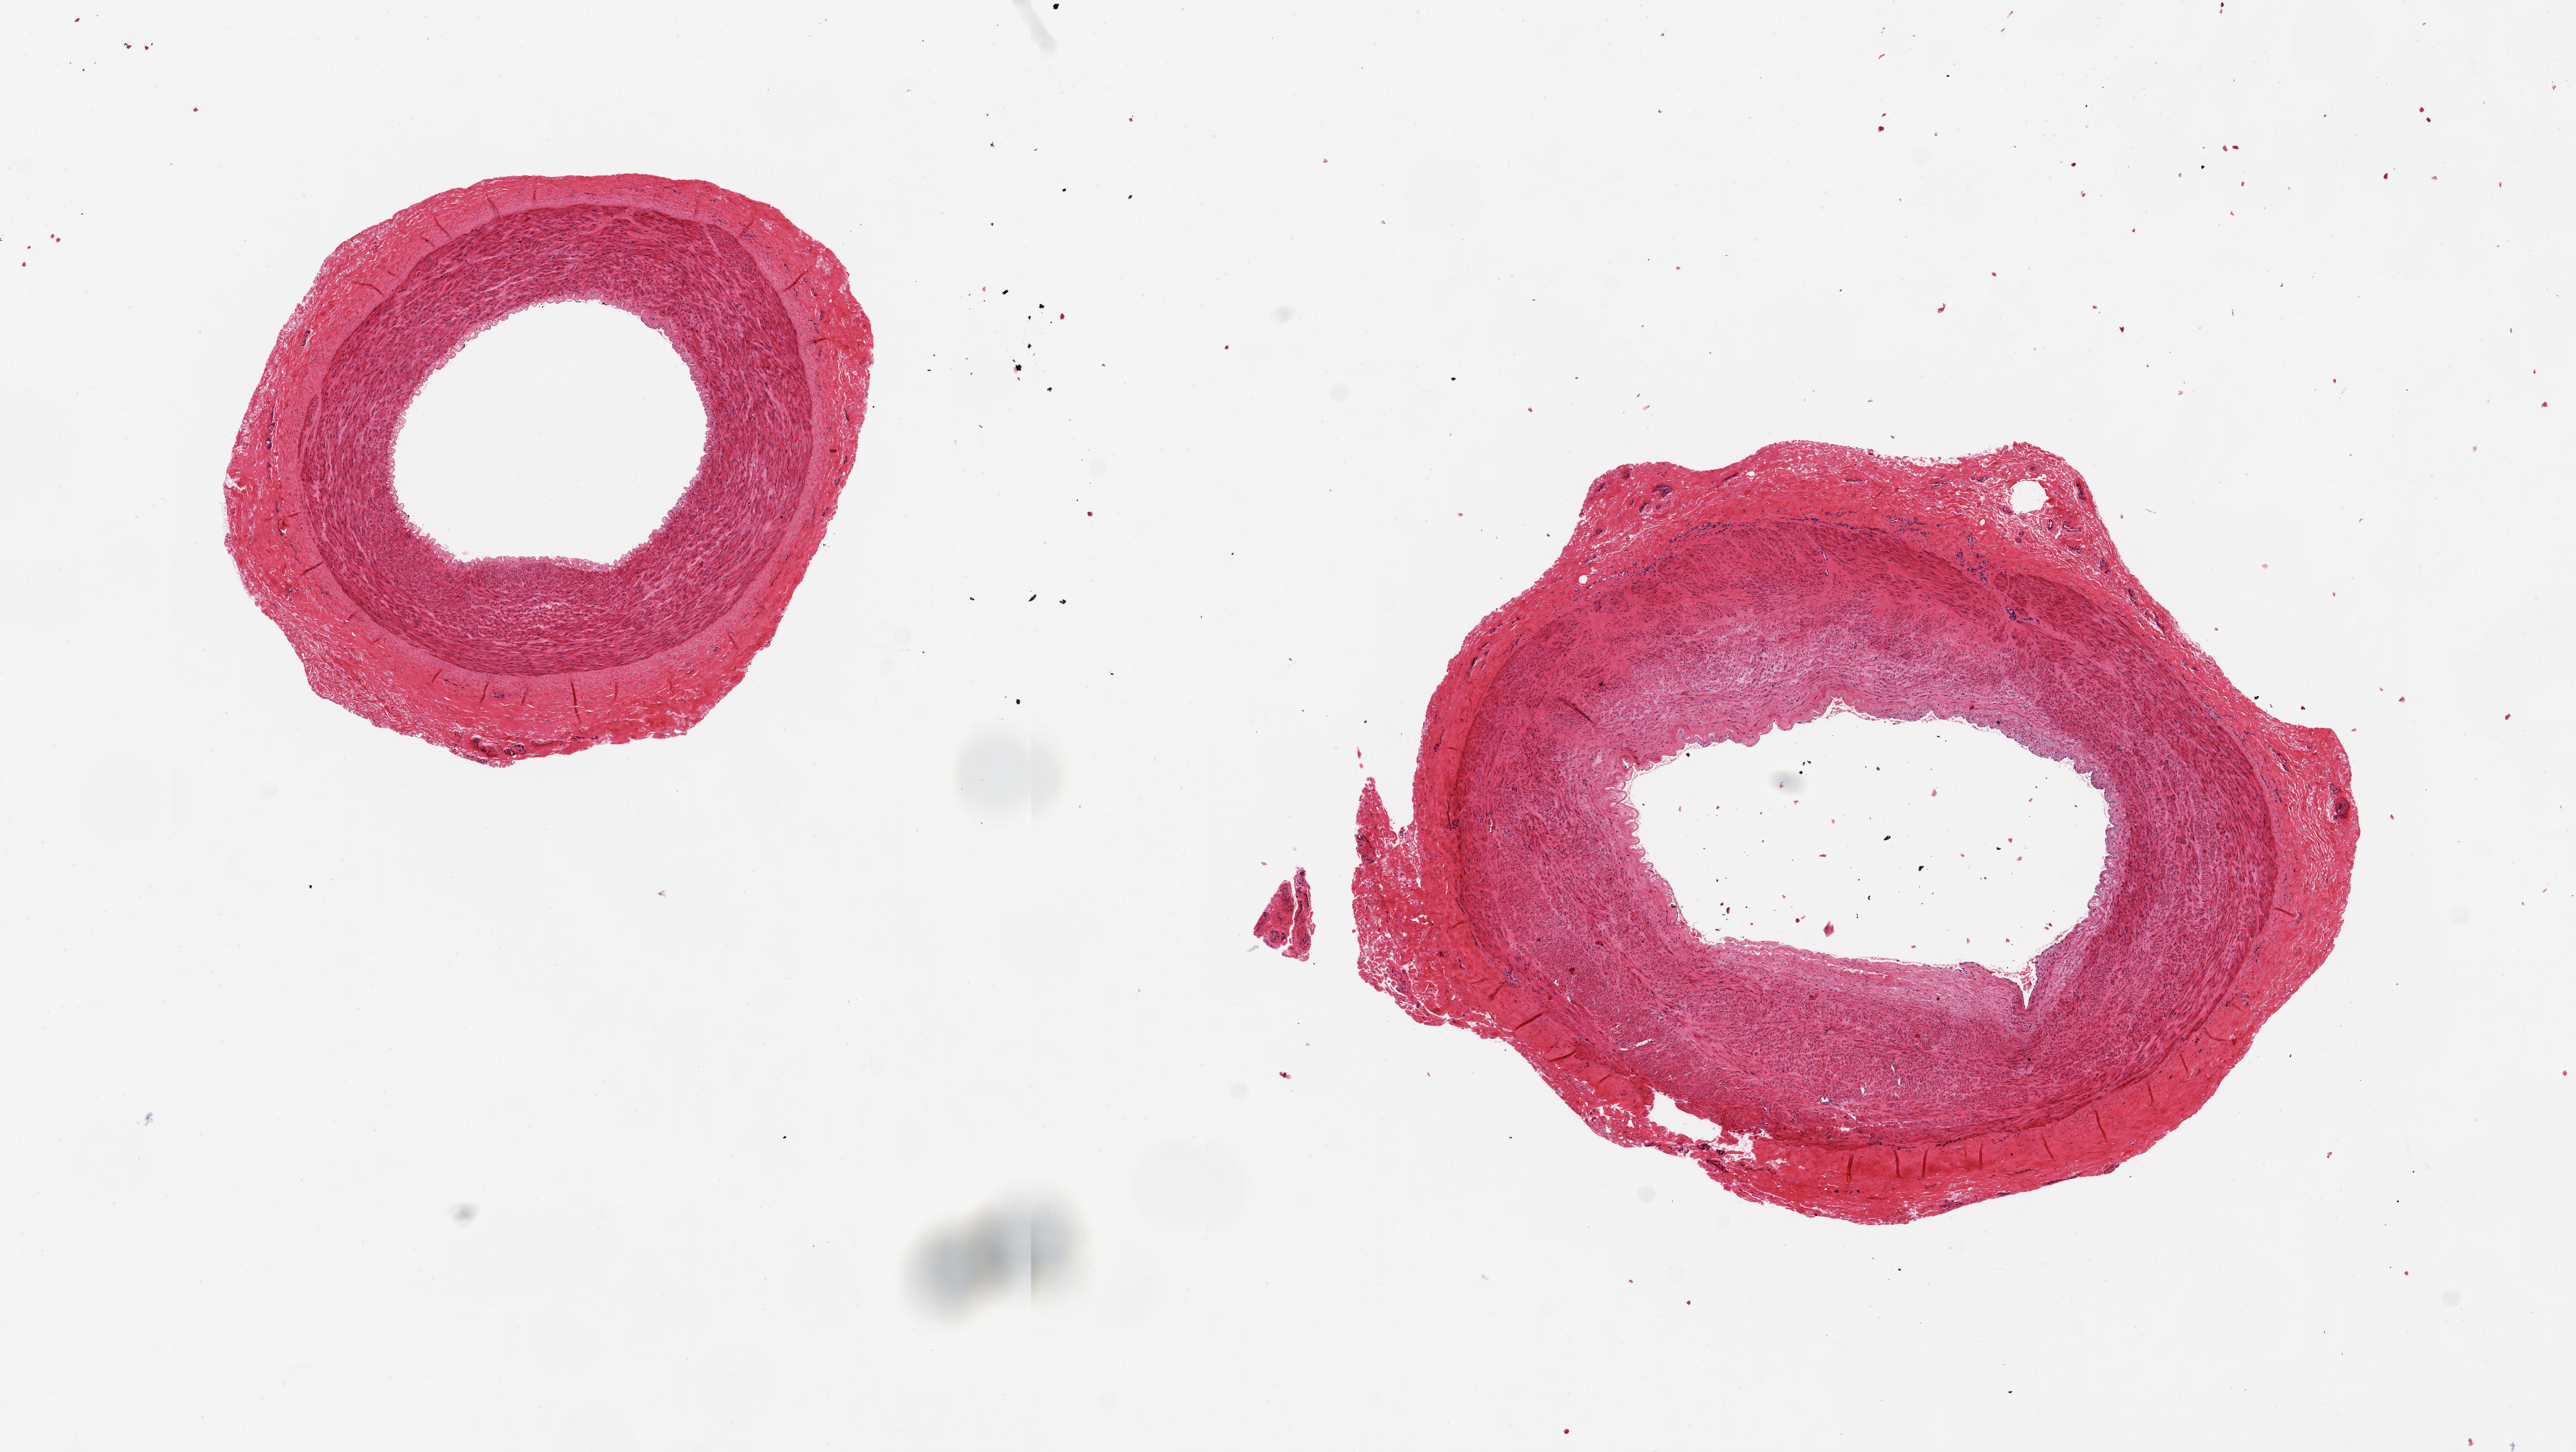
Digitized haematoxylin and eosin-stained section, low-resolution overview of the scanned area, about 14.8 x 8.3 mm; PAXgene-fixed, paraffin-embedded tissue; section of tibial artery (target tissue); tissue donor sample. Male donor.
* reviewer comment on this tissue sample: 2 pieces, good clean specimens, ~4mm d. No atherosis